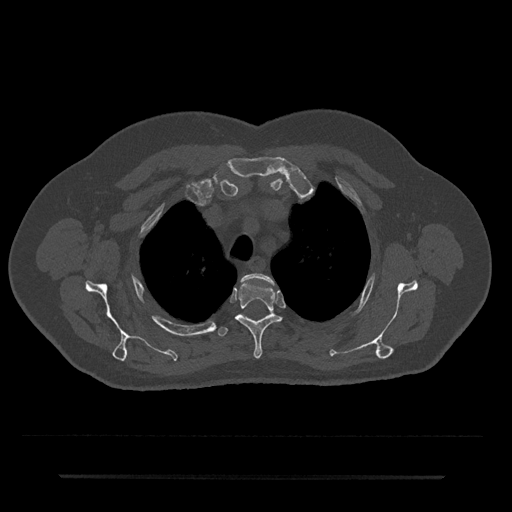
CT including the spine, one axial slice; position 565 of 797 along the scan axis; reconstruction kernel Br40s/3; 120 kVp; bone window (W 1800 / L 400 HU); 0.5 mm slice thickness; 512 × 512 image matrix. Patient: male, 69 years. Case-level facts recorded for this patient, not image findings: primary cancer: prostate.
Outlined on this slice (semi-automatically segmented with operator editing):
- T2 vertebra: bounding box (x1, y1, x2, y2) in pixels: (242, 273, 274, 284)
- T3 vertebra: (235, 281, 281, 359)
- T4 vertebra: (218, 327, 228, 337)